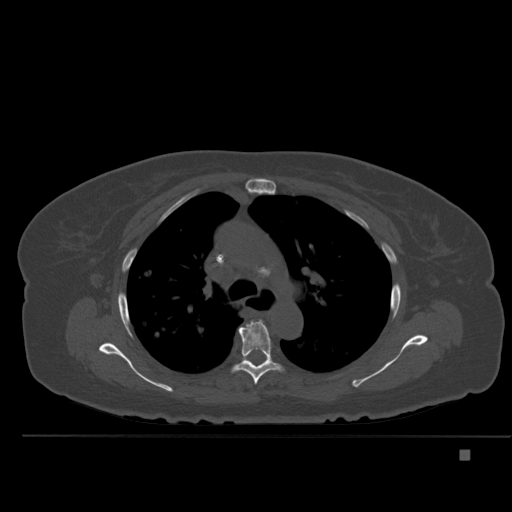
CT including the spine, one axial slice; bone window (W 1800 / L 400 HU); 1.5 mm slice thickness; 512 × 512 image matrix, field of view 422 × 422 mm. Female patient, age 74 years. Case-level facts recorded for this patient, not image findings: primary cancer: colon.
Structures marked on this image (semi-automatically segmented with operator editing):
- T5 vertebra: bounding box (x1, y1, x2, y2) in pixels: (233, 320, 282, 385)